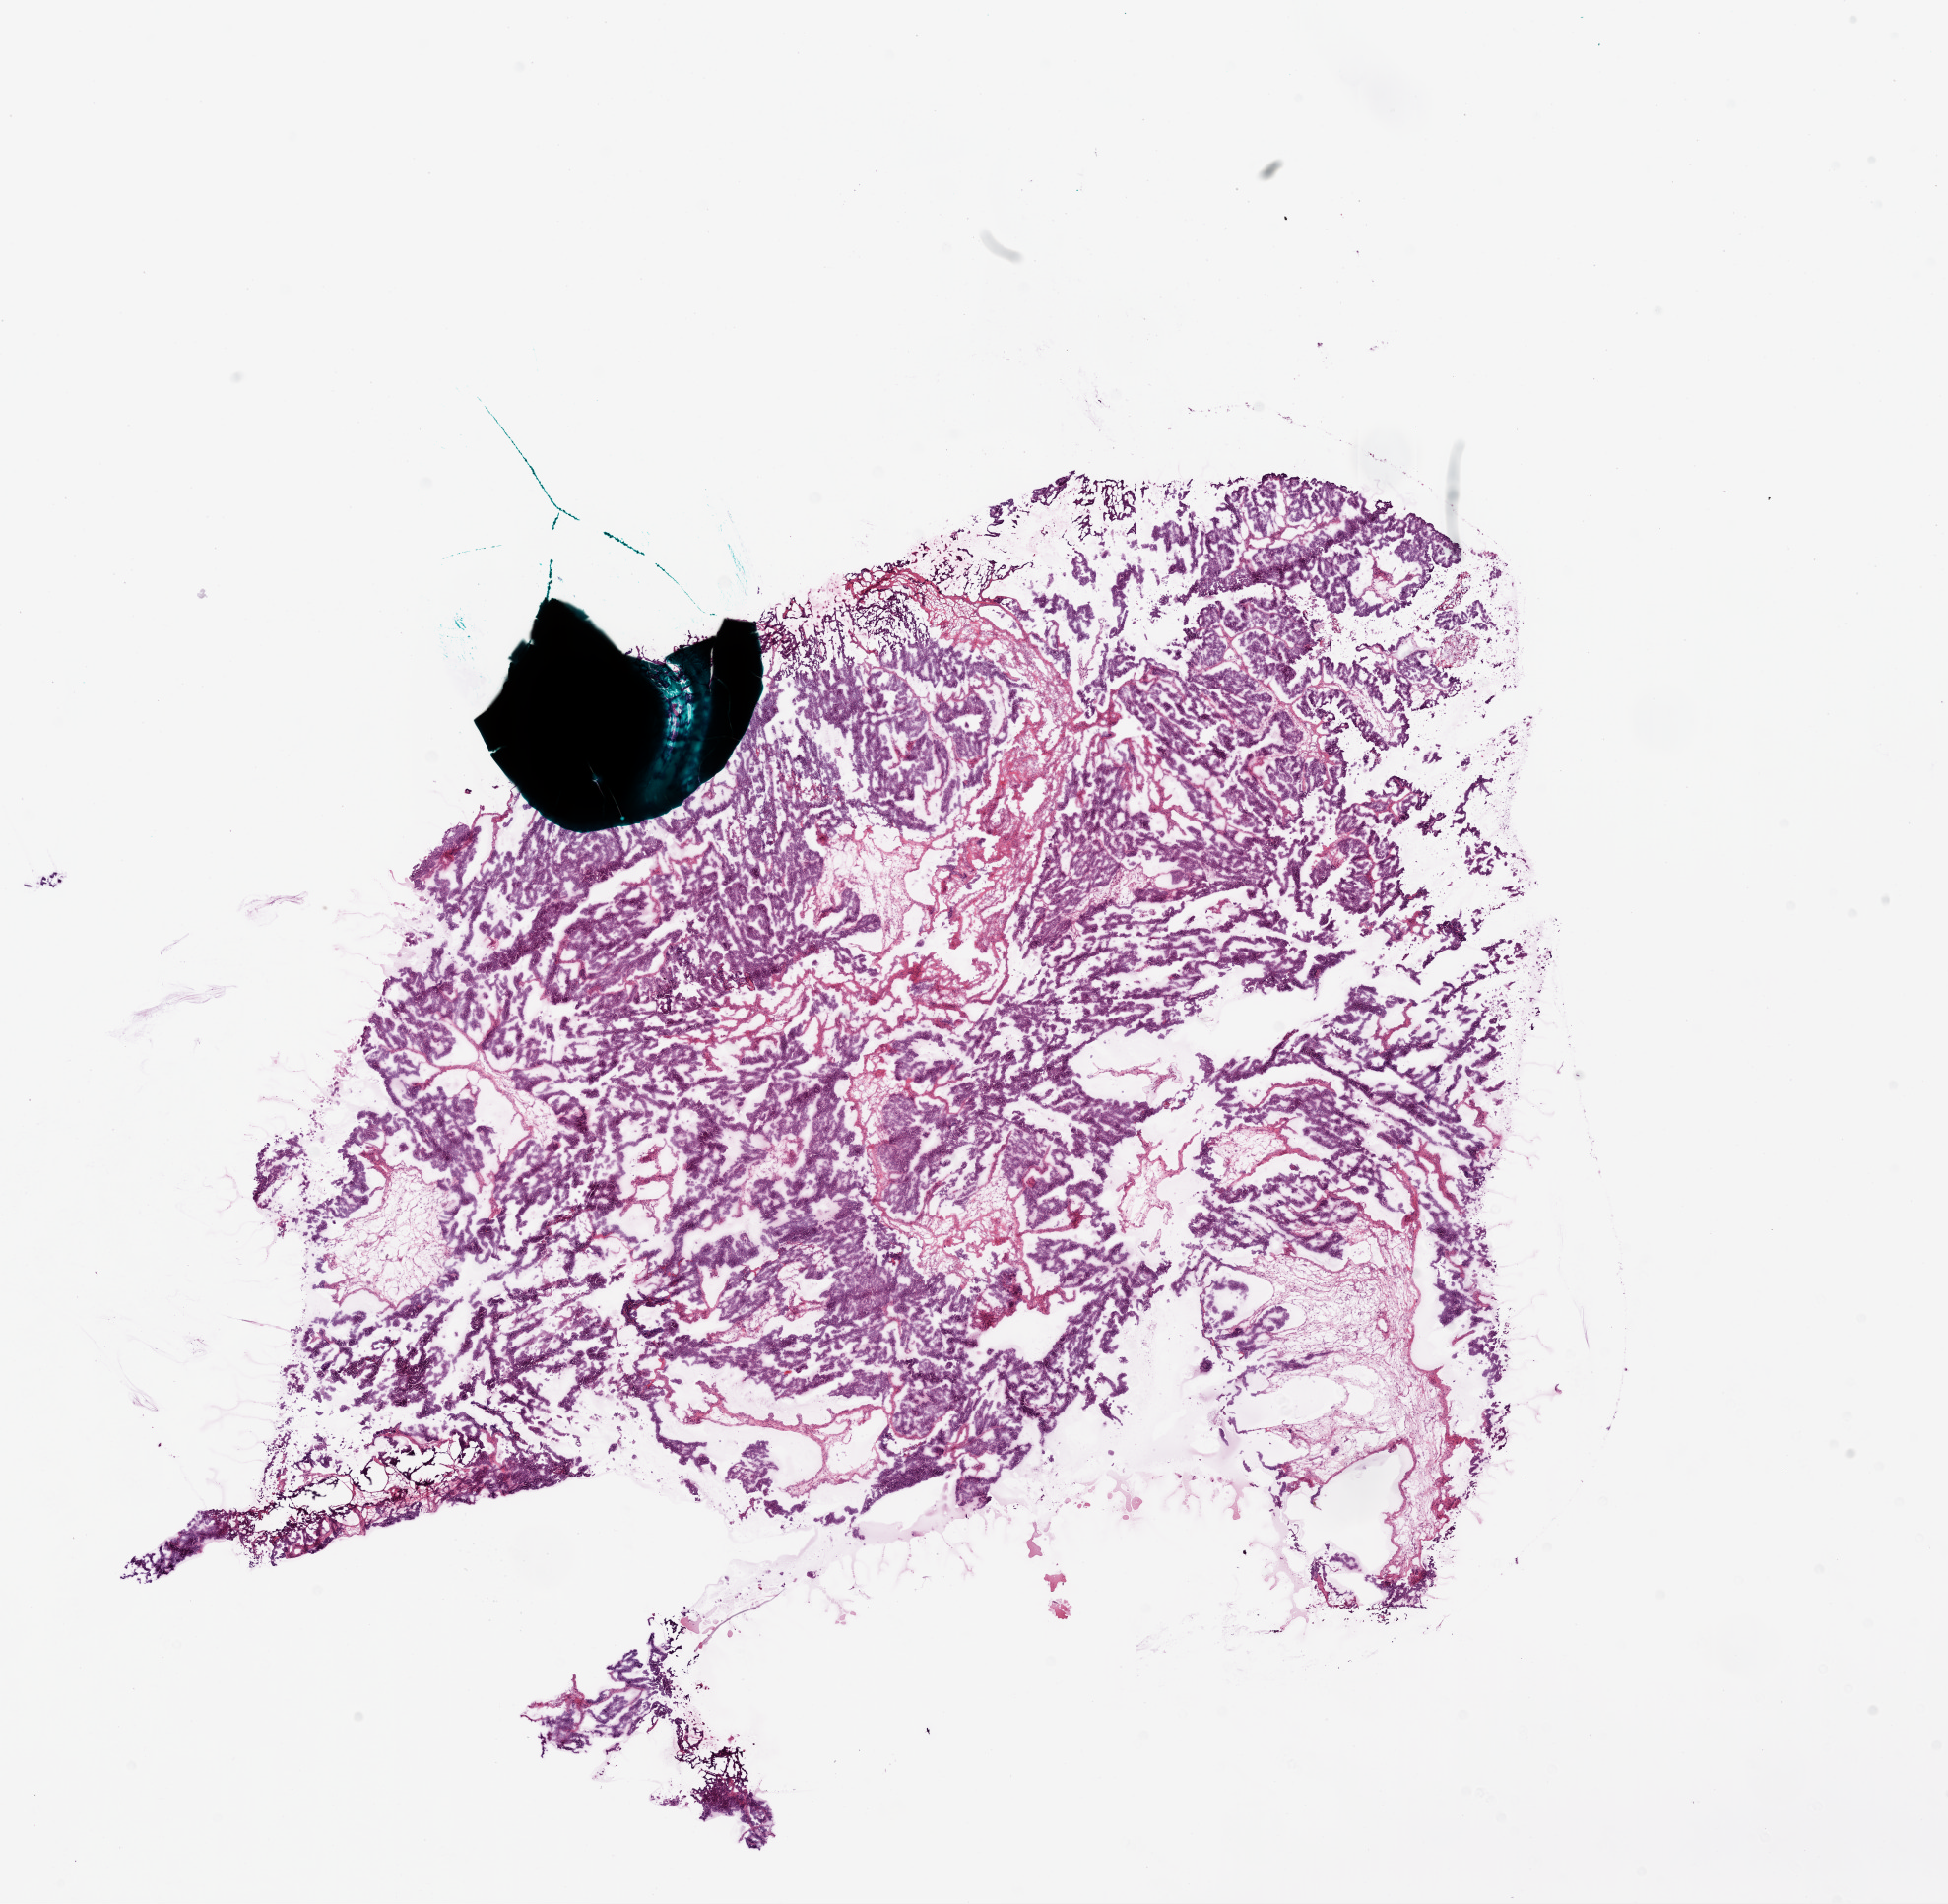
Digitized H&E tissue section (whole slide), low-resolution overview of the scanned area, about 16.0 x 15.6 mm (acquisition: 20x scan), frozen section from the bottom of the tissue portion, sample: primary tumour, ovary. Female patient; age at initial diagnosis 80 years. Histologic grade: G3 (poorly differentiated). Pathologist review of this section (percent, as recorded): tumour cells 80%, tumour nuclei 80%, normal cells 5%, stromal cells 15%, necrosis 0%.
Pathologic diagnosis: Serous cystadenocarcinoma, NOS. FIGO stage: IIIC. Laterality: bilateral.